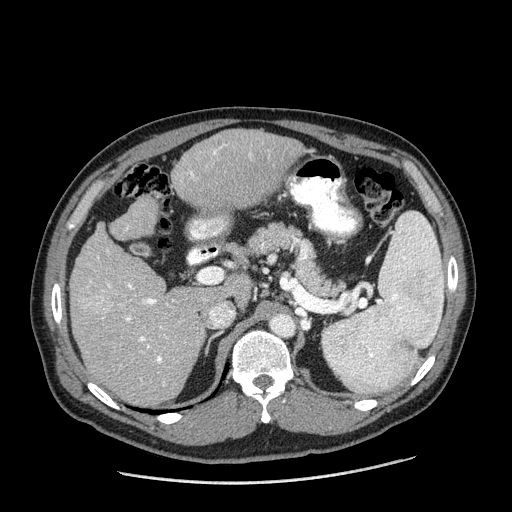
Contrast-enhanced abdominal CT (liver protocol), one axial slice. Slice 107 of 198 in the series (ordered by position). 120 kVp. One of 2 acquisitions stored at this slice position. Soft-tissue window (W 400 / L 40 HU). 512 × 512 image matrix, field of view 400 × 400 mm. From the clinical record (not read from this slice): diagnosis: hepatocellular carcinoma (patient treated with transarterial chemoembolisation; whether this scan precedes or follows treatment is not stated here); TNM stage (as recorded): Stage-II; Child-Pugh class: A; tumour differentiation: moderately differentiated; tumour nodularity: multinodular.
Annotated regions visible in this slice (semi-automatic segmentation, software-assisted and operator-edited):
- liver parenchyma outside the tumour (the mass and vessels are separate outlines, so this box may not span the whole liver): bounding box <69,128,304,406> (left, top, right, bottom; pixels)
- mass: <81,292,113,316>
- liver vessels: <107,150,251,380>